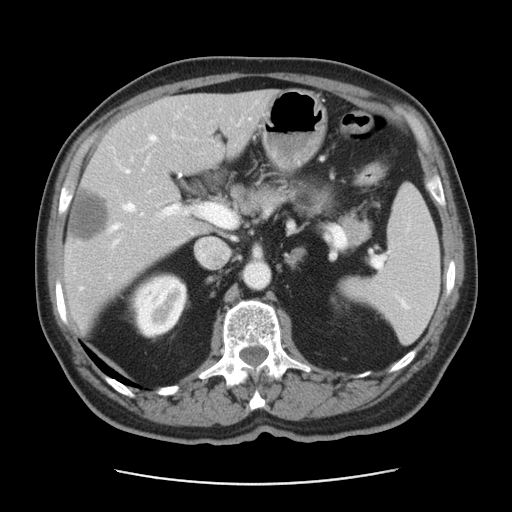
Contrast-enhanced abdominal CT, one axial slice. 120 kVp. Intravenous contrast given. Soft-tissue window (W 400 / L 40 HU). 512 × 512 image matrix. Male patient, age 73 years. Case-level facts recorded for this patient, not image findings: diagnosis: colorectal cancer liver metastases, imaged before liver resection; multiple liver metastases: yes; largest metastasis: 0.5 cm; disease in both lobes: no.
Structures marked on this image (outlined manually by an expert reader):
- hepatic veins: bounding box (x1, y1, x2, y2) in pixels: (80, 136, 155, 290)
- liver: (65, 93, 272, 330)
- planned liver remnant (the part of the liver to remain after resection): (110, 92, 271, 230)
- portal vein (with intrahepatic branches): (114, 171, 223, 244)
- liver metastasis: (70, 192, 108, 241)